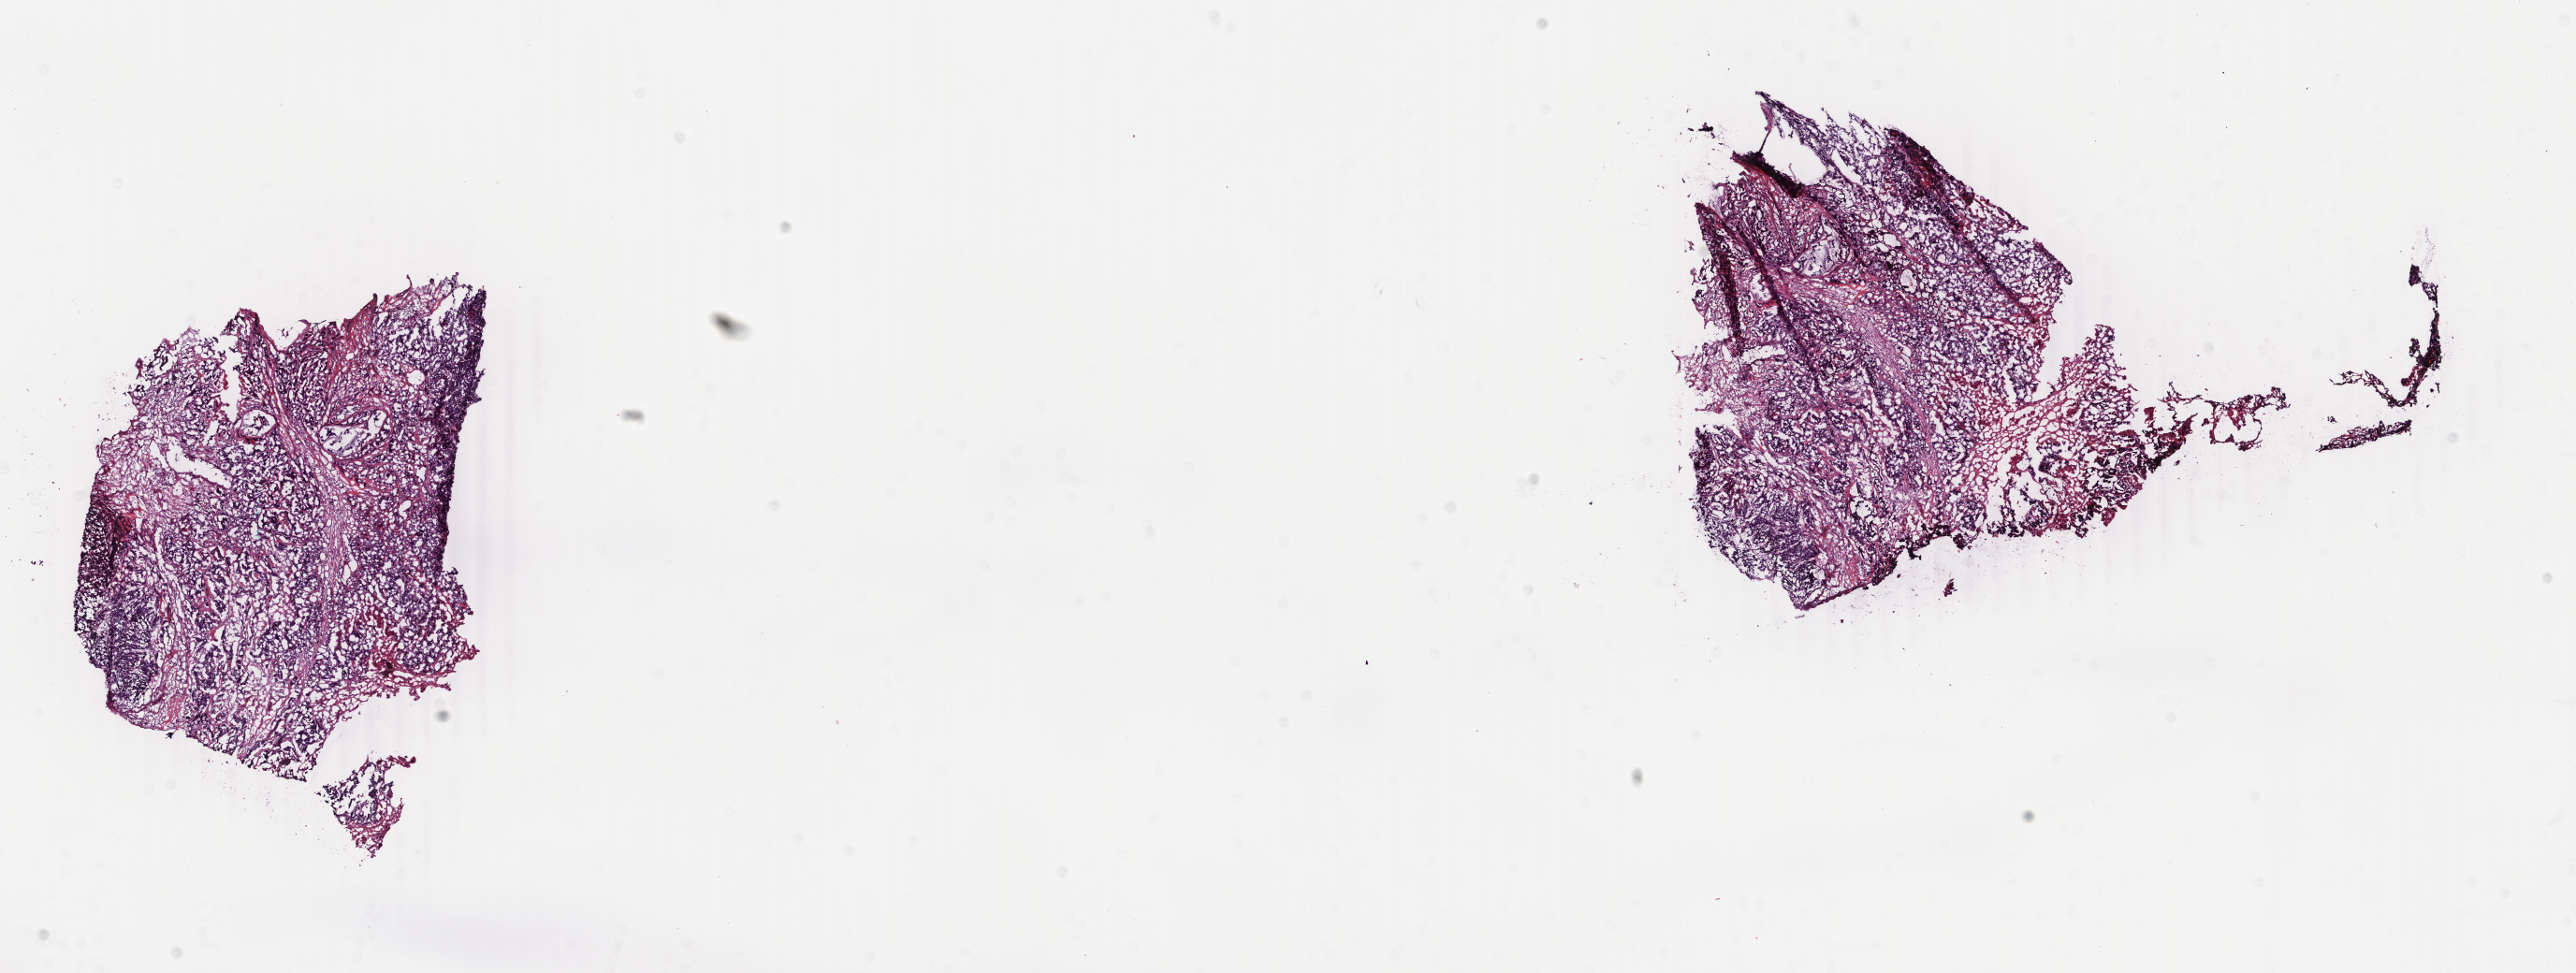
Whole-slide histology image, H&E, a low-resolution overview of the entire scanned area, about 21.9 x 8.3 mm. Frozen section. Breast, primary tumour sample. Female, age 40 years at initial diagnosis. Pathologist review of this section (percent, as recorded): tumour cells 95%, tumour nuclei 85%, normal cells 0%, stromal cells 5%, necrosis 0%. Infiltration values recorded for this section: lymphocyte infiltration 0%, monocyte infiltration 0%, neutrophil infiltration 0%.
TNM: T1c N0 (i-) M0. Laterality: right. Diagnosis: Infiltrating duct mixed with other types of carcinoma. AJCC pathologic stage: IA (3rd edition). Lymph nodes positive (case pathology): 0 of 15 examined.